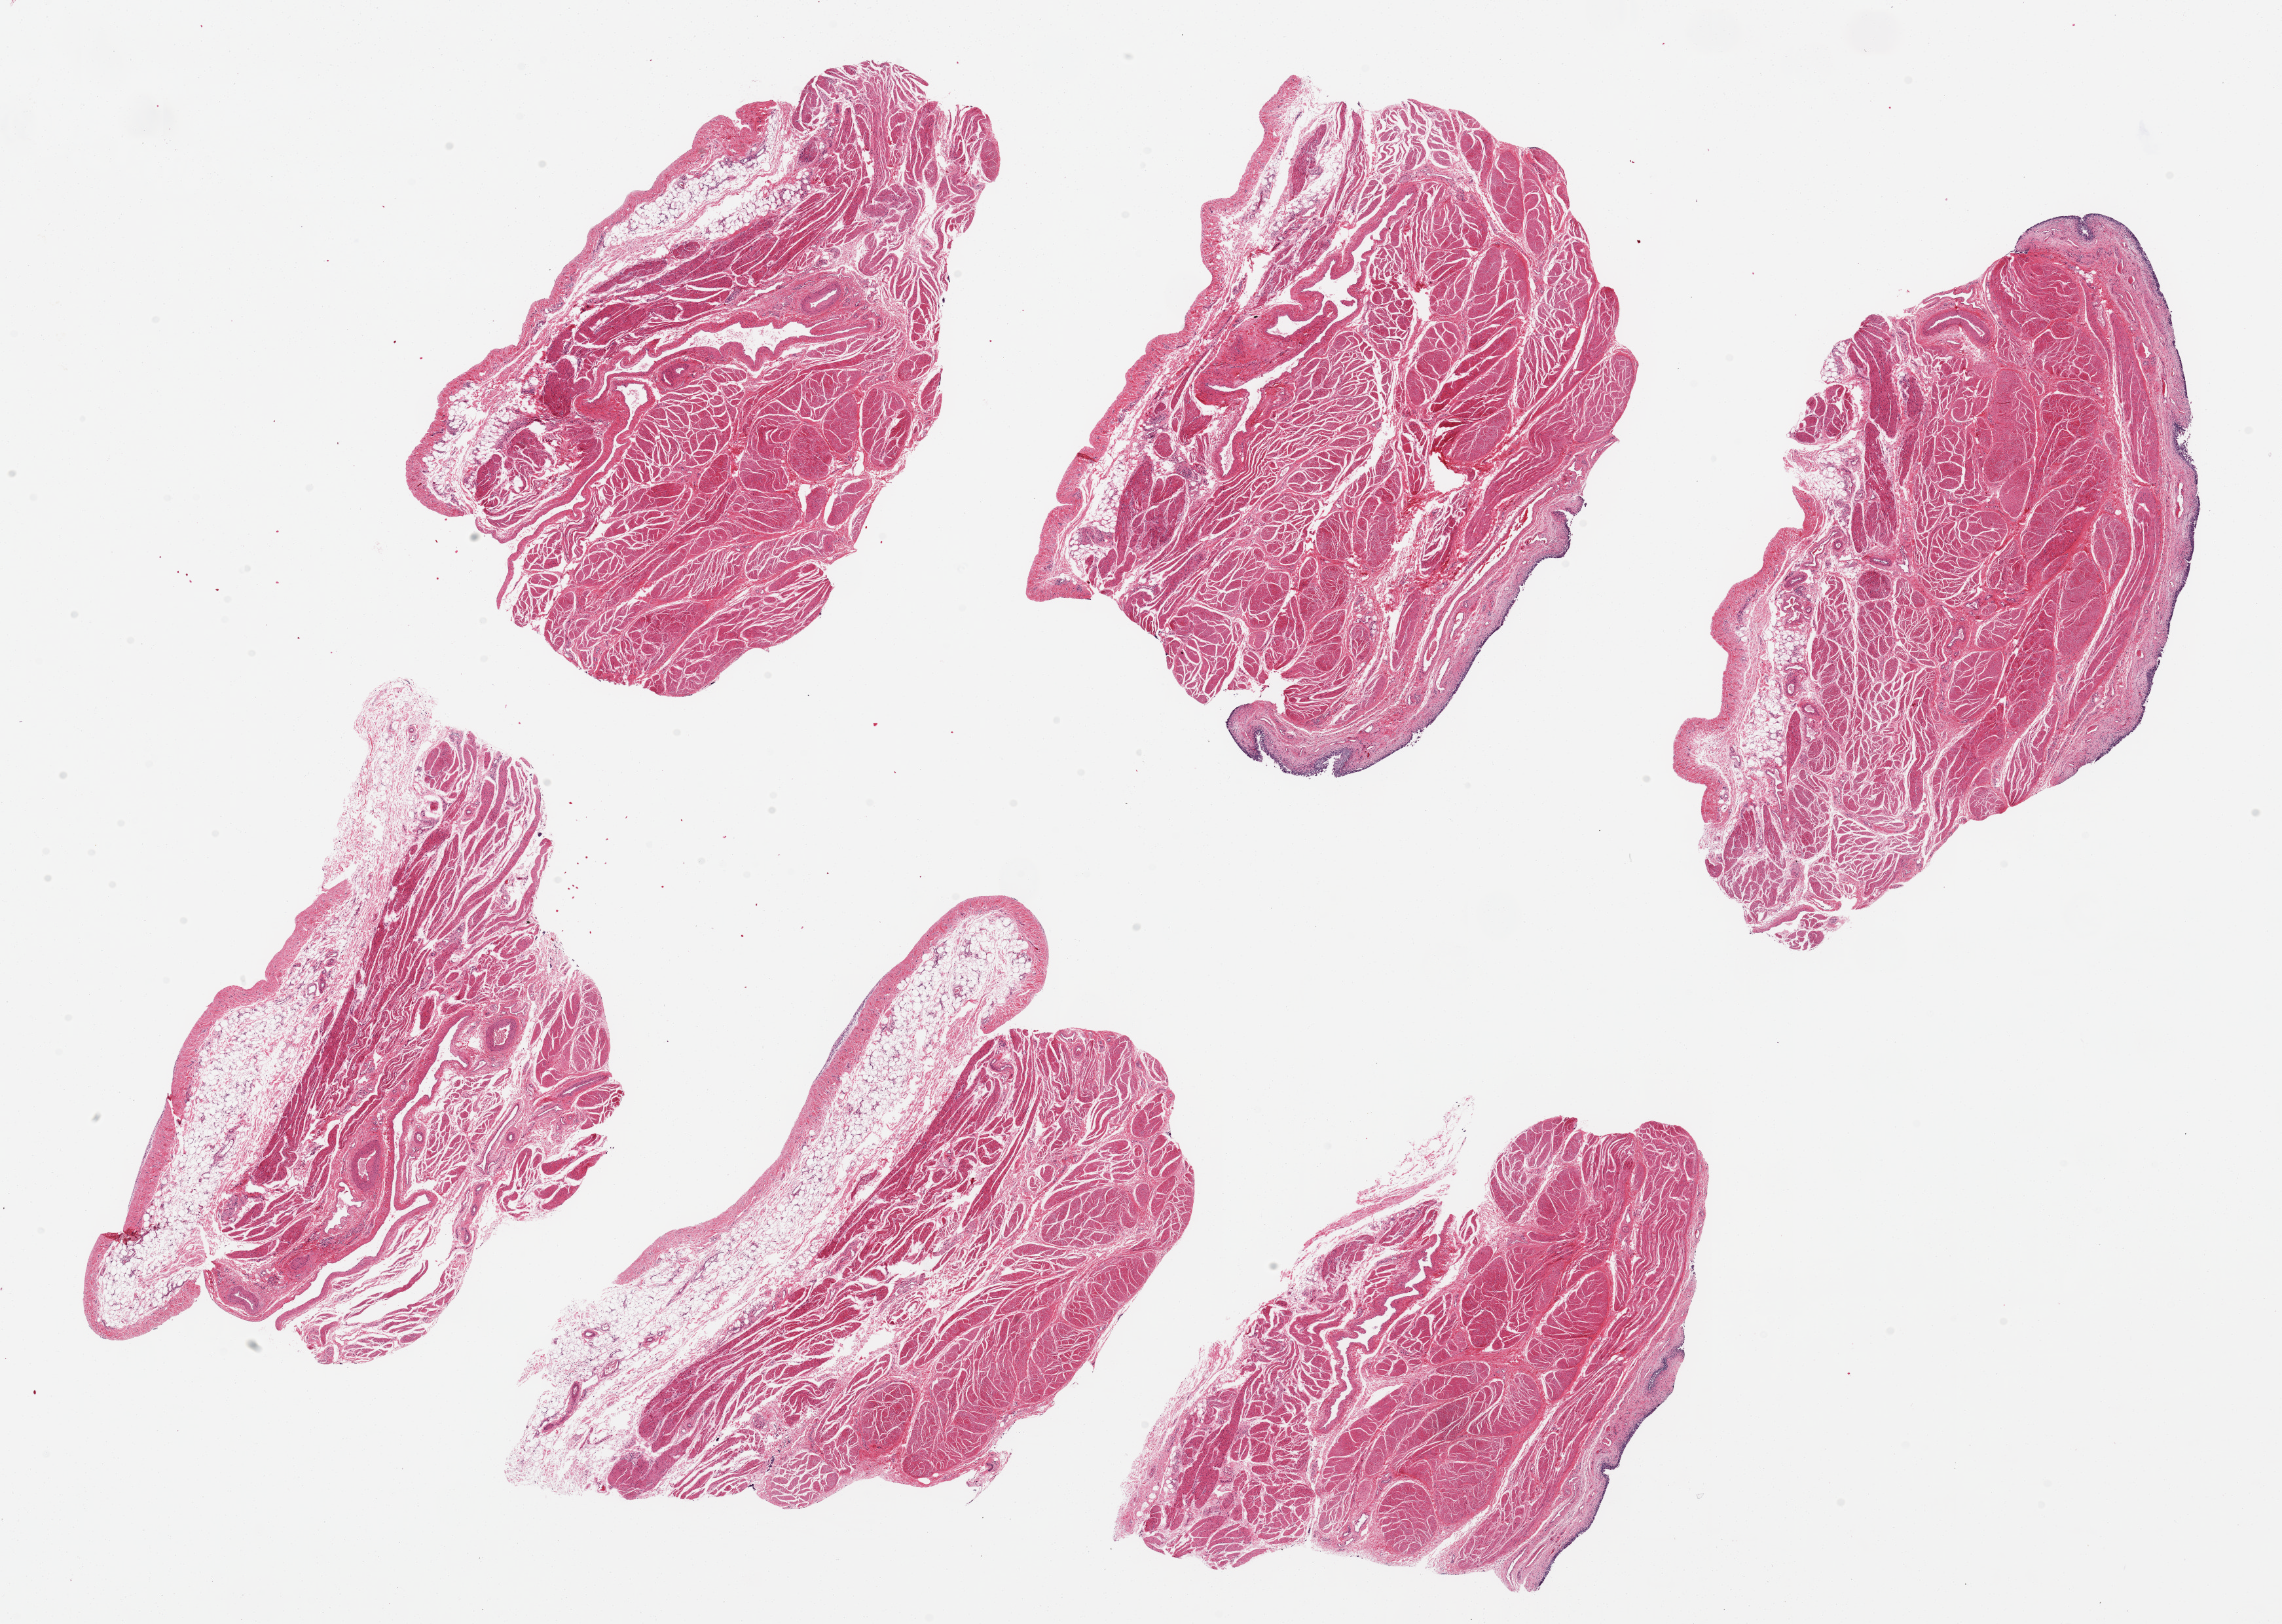
Digitized H&E-stained section, brightfield, low-resolution overview of the scanned area, about 27.6 x 19.6 mm, PAXgene-fixed paraffin-embedded (PFPE) section, sampled site (target tissue): urinary bladder, donor tissue sample. Female donor.
* pathologist's review note for this sample: 6 ~8x5mm pieces. Urotherlium nearly completely sloughed; muscularis/adipose tissue is >99% of sections